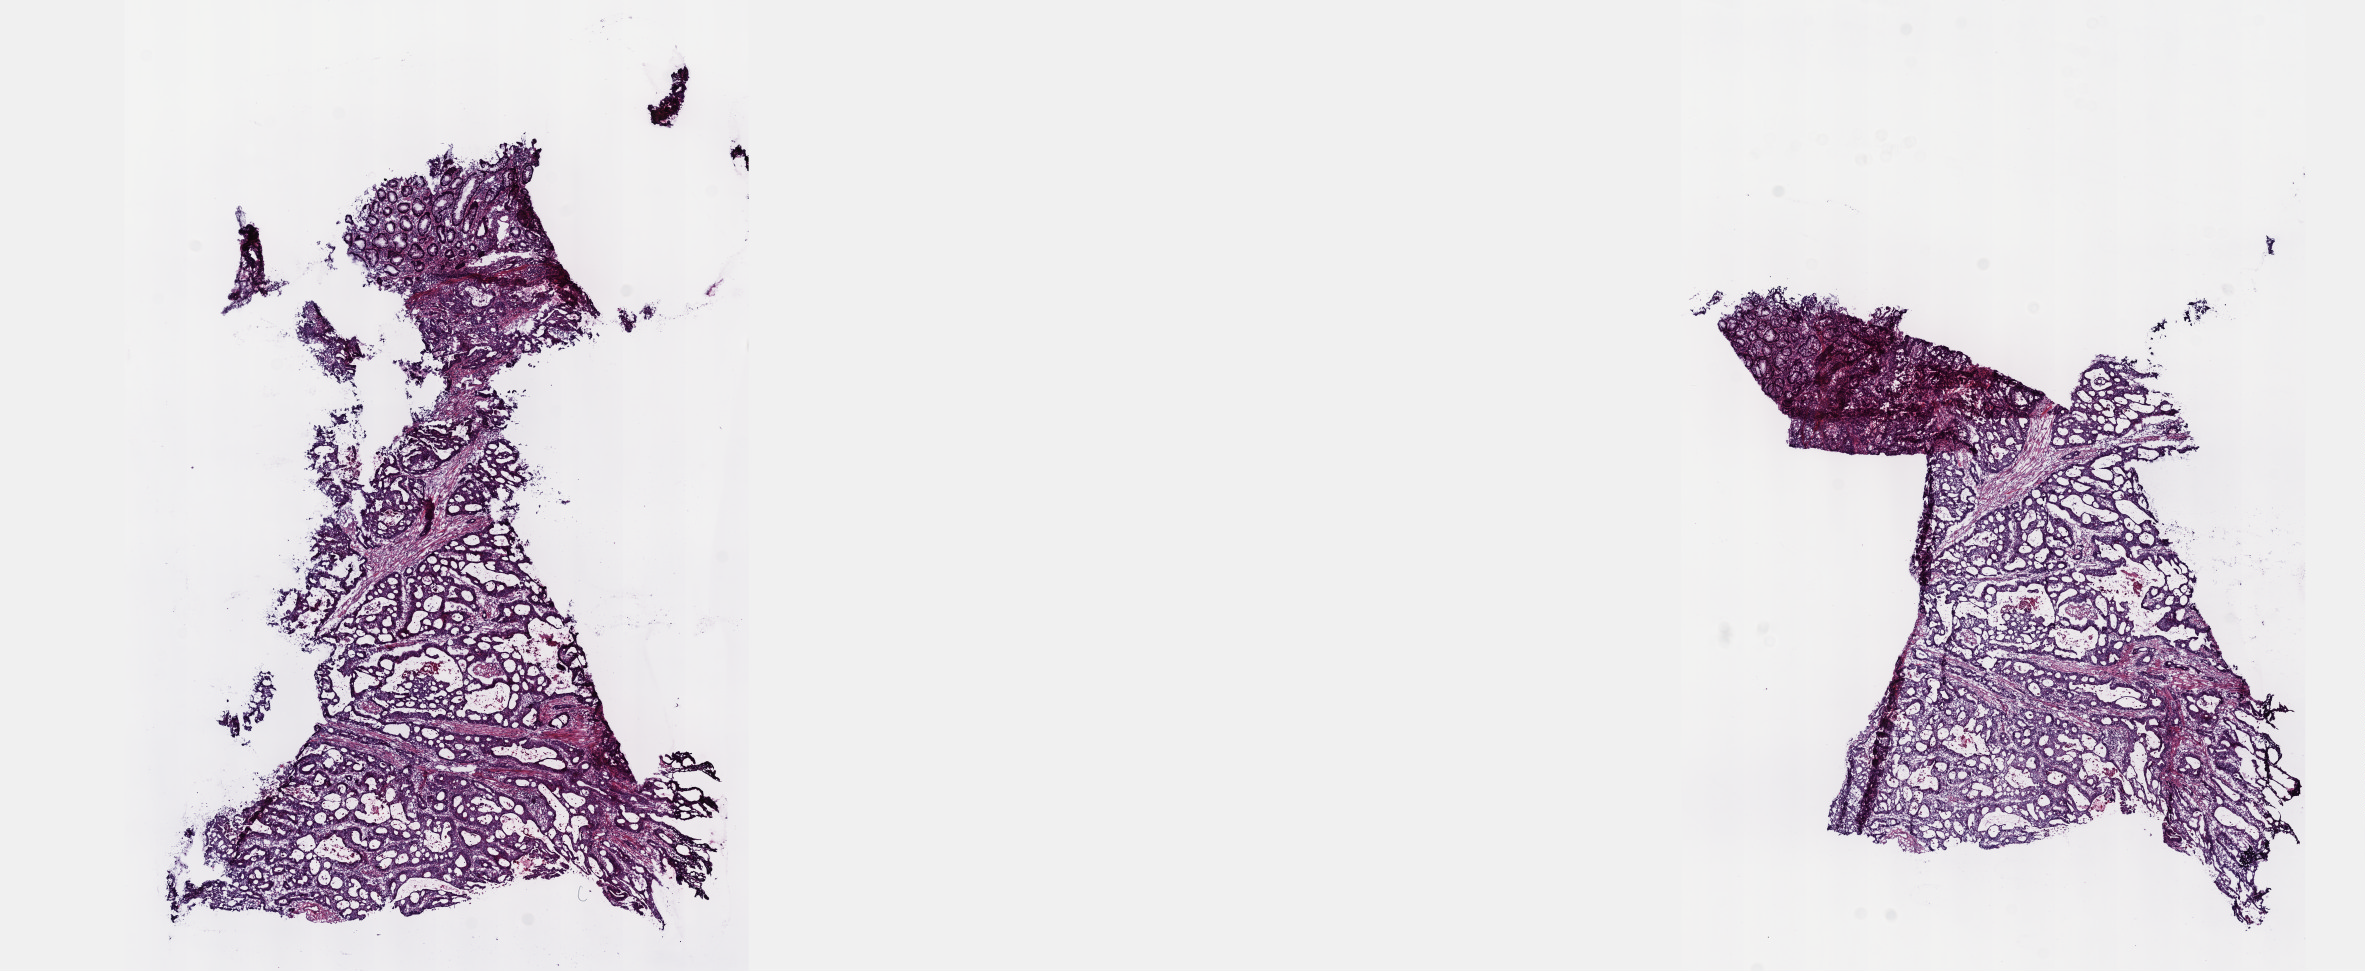
Digitized H&E-stained tissue section (whole slide) — low-resolution overview of the scanned area, about 19.1 x 7.8 mm. Frozen section from the top of the tissue portion. Sample: primary tumour, colon. Male patient; age at initial diagnosis 67 years. Pathologist review of this section (percent, as recorded): tumour cells 45%, tumour nuclei 75%, normal cells 10%, stromal cells 35%, necrosis 10%. Inflammatory infiltration, as recorded: lymphocyte infiltration 12%, monocyte infiltration 4%, neutrophil infiltration 4%.
* AJCC pathologic stage: IIIB
* lymph nodes positive (case pathology): 2 of 25 examined
* histologic diagnosis: Adenocarcinoma, NOS (ascending colon)